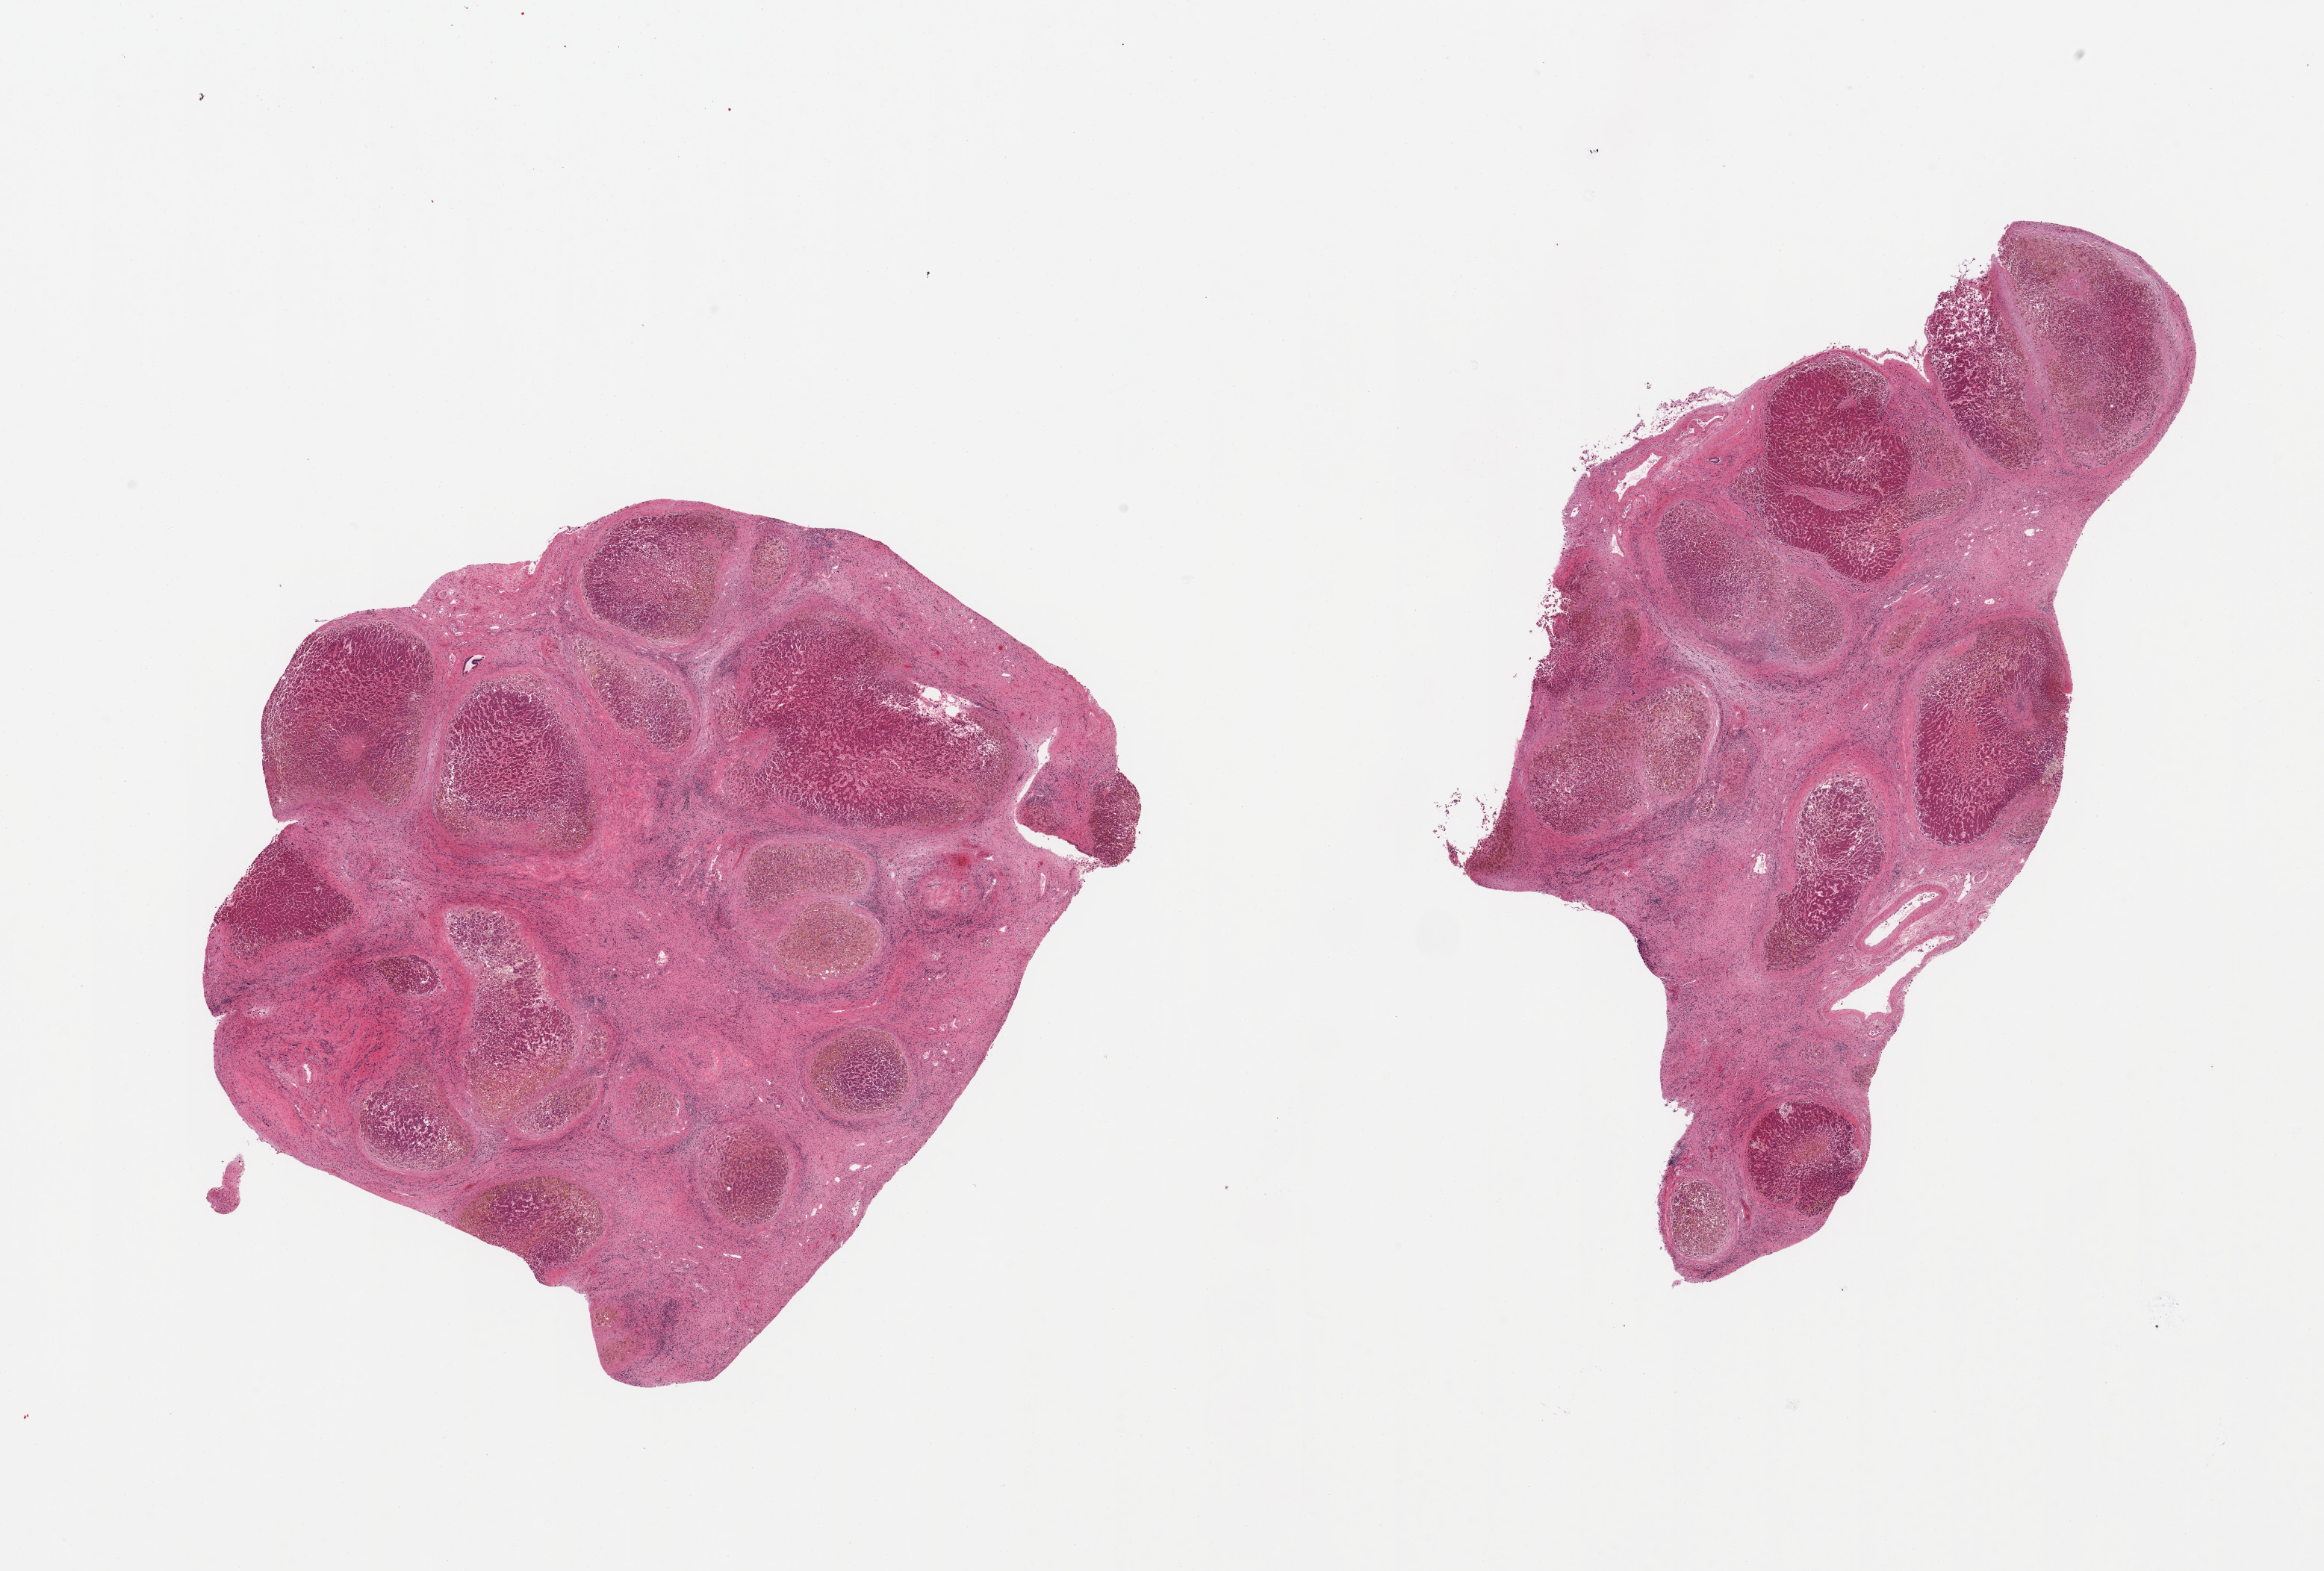
Digitized haematoxylin and eosin-stained section — shown as a low-resolution overview of the whole scanned area (about 24.6 x 16.6 mm, from a 20x scan), PAXgene-fixed paraffin-embedded (PFPE) section, section of liver (target tissue), tissue donor sample. Female donor.
Review note (as recorded): 2 pieces; cirrhosis, chronic inflammation, Mallory's hyaline, bile pigment and hepatocyte degeneration/necrosis.